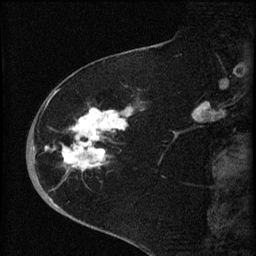
Breast MRI (dynamic contrast-enhanced), one sagittal slice; position 23 of 60 along the scan axis; dynamic contrast-enhanced series, image 2 of 4 at this slice position (ordered by acquisition); 1.5 T; TE 4.2 ms, TR 8.2 ms; 256 × 256 image matrix, field of view 180 × 180 mm. Patient: female, 71 years.
Structures marked on this image (semi-automatically segmented with operator editing):
- analysis volume of interest (the breast-tissue region the enhancement analysis was run in; not a lesion): bounding box [x1, y1, x2, y2] px = [35, 75, 147, 190]
- tumour enhancement mask (voxels above the 70 % enhancement threshold inside the analysis volume of interest): [46, 91, 133, 172]